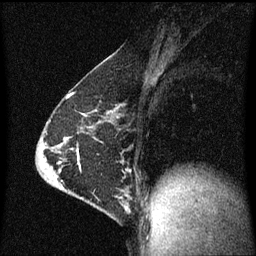
Breast MRI (dynamic contrast-enhanced), one sagittal slice. Position 37 of 60 along the scan axis. Dynamic contrast-enhanced series, image 2 of 3 at this slice position (ordered by acquisition). 1.5 T. TE 4.2 ms, TR 8 ms. 2 mm slice thickness. 256 × 256 image matrix. Female patient, age 64 years.
Structures marked on this image (semi-automatic segmentation, software-assisted and operator-edited):
- analysis volume of interest (the breast-tissue region the enhancement analysis was run in; not a lesion): bounding box <87,188,130,217> (left, top, right, bottom; pixels)
- tumour enhancement mask (voxels above the 70 % enhancement threshold inside the analysis volume of interest): <121,198,127,211>